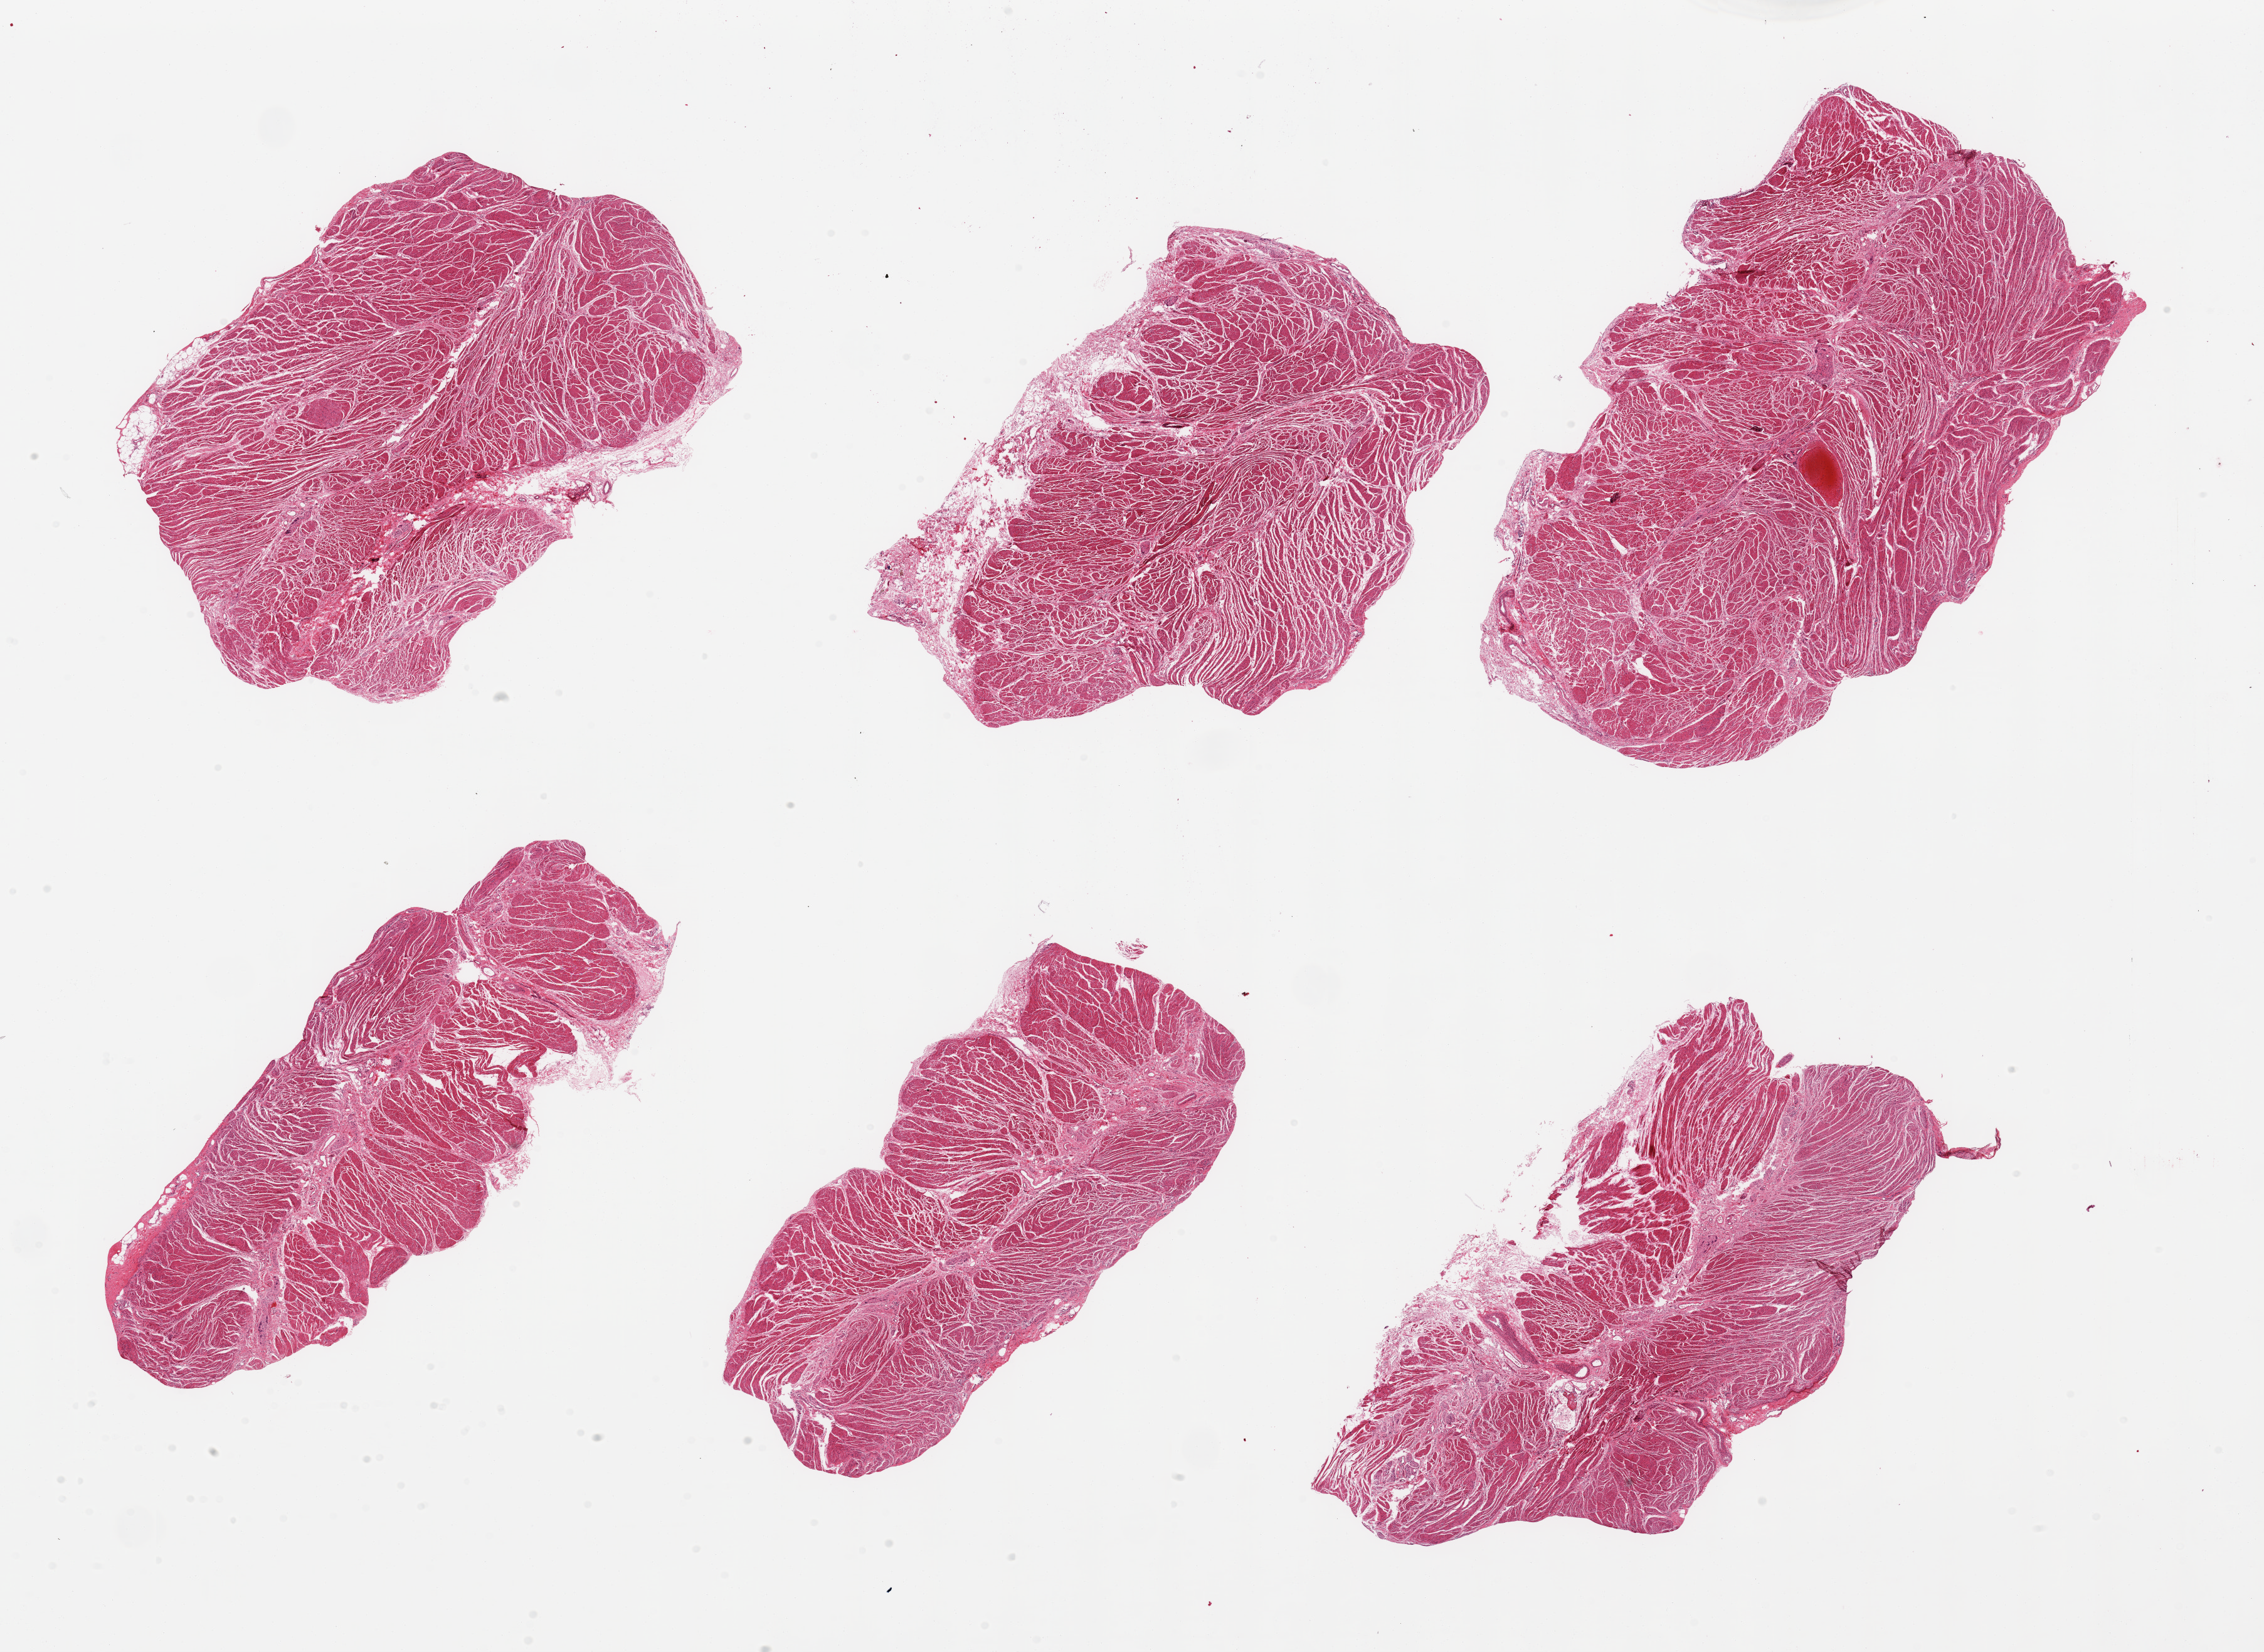
Digitized hematoxylin and eosin (H&E)-stained section — shown as a low-resolution overview of the whole scanned area (about 28.5 x 20.8 mm, acquisition: 20x scan), PAXgene-fixed, paraffin-embedded tissue, sampled site (target tissue): gastroesophageal junction, tissue donor sample.
Reviewer comment on this tissue sample: 6 pieces; target muscularis.